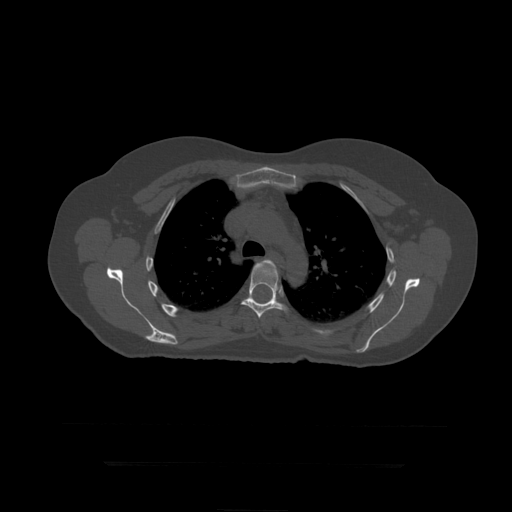
CT including the spine, one axial slice; slice 321 of 399 in the series (ordered by position); 120 kVp; bone window (W 1800 / L 400 HU); 1.25 mm slice thickness; 512 × 512 image matrix, field of view 450 × 450 mm. Patient age 41 years. From the clinical record (not read from this slice): primary cancer: breast.
Structures marked on this image (semi-automatically segmented with operator editing):
- T5 vertebra: box from (x=258, y=260) to (x=276, y=268) px
- T6 vertebra: (x=241, y=263)–(x=288, y=319)